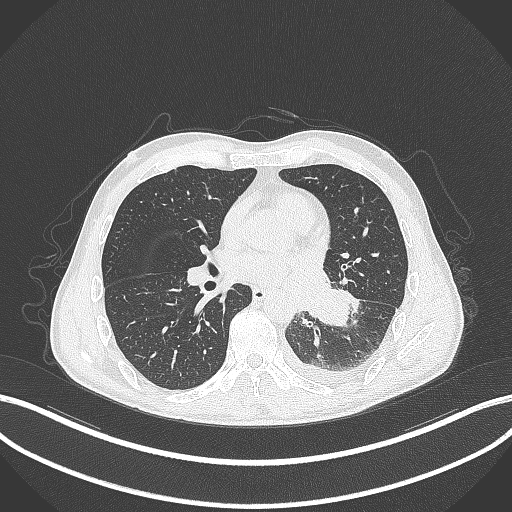
Chest CT, one axial slice. Position 150 of 295 along the scan axis. 120 kVp. Lung window (W 1500 / L -600 HU). 1 mm slice thickness. 512 × 512 image matrix. Patient: male, 47 years. Case-level facts recorded for this patient, not image findings: clinical TNM (as recorded): T3 N1 M1c.
Annotated regions visible in this slice (bounding box drawn by a radiologist):
- lung tumour (recorded histology: small cell carcinoma): bounding box <307,288,351,328> (left, top, right, bottom; pixels)